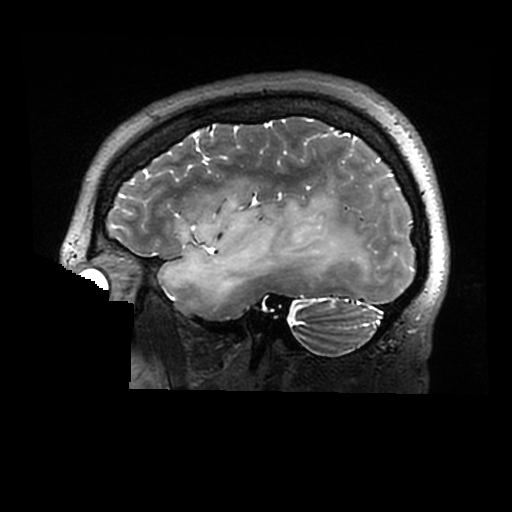
Brain MRI from a brain-tumour surgery series, one sagittal slice. Slice 221 of 320 in the series (ordered by position). 512 × 512 image matrix. Case-level facts recorded for this patient, not image findings: histopathology: Astrocytoma; WHO grade: 2; IDH mutation: yes.
Annotated regions visible in this slice (manually delineated by an expert):
- tumour: bounding box (x1, y1, x2, y2) in pixels: (158, 194, 378, 306)